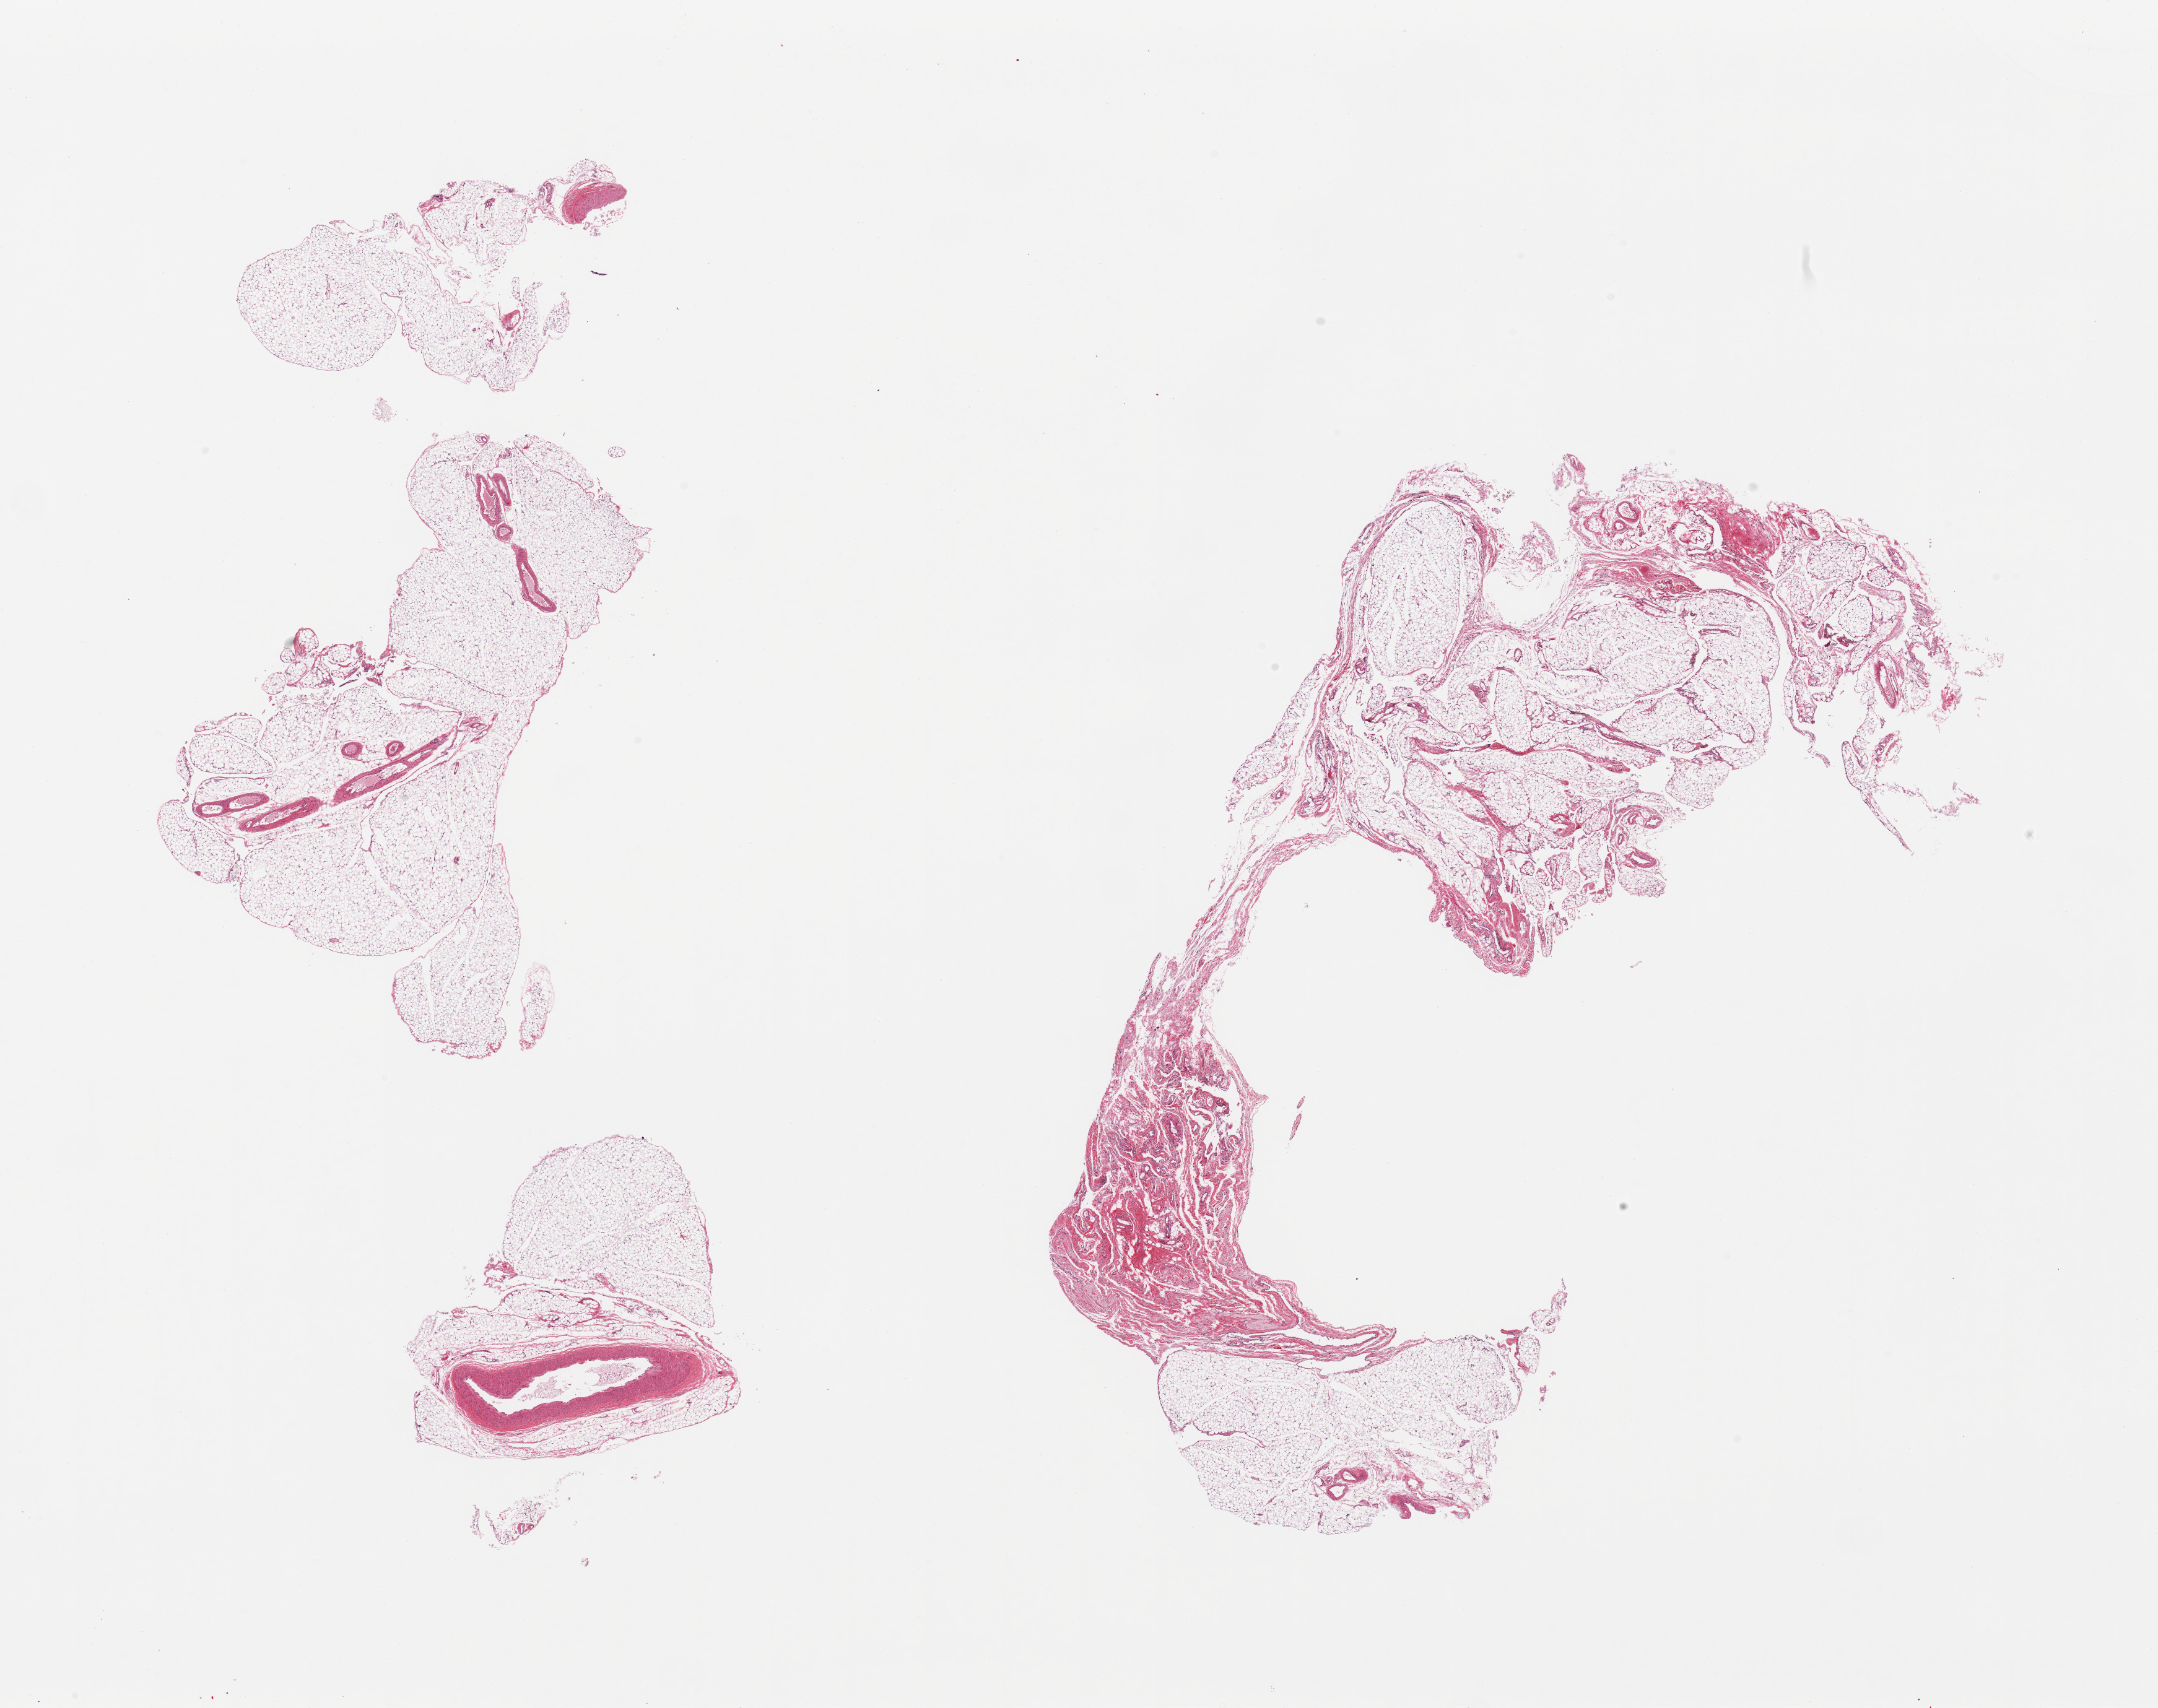
Digitized H&E-stained section, whole scanned area (about 27.6 x 21.8 mm, acquisition: 20x scan) shown as a low-resolution overview. PAXgene-fixed paraffin-embedded (PFPE) section. Sampled site (target tissue): omentum. Tissue donor sample. Donor: male.
• reviewer comment on this tissue sample: 2 pieces, trace mononuclear cells